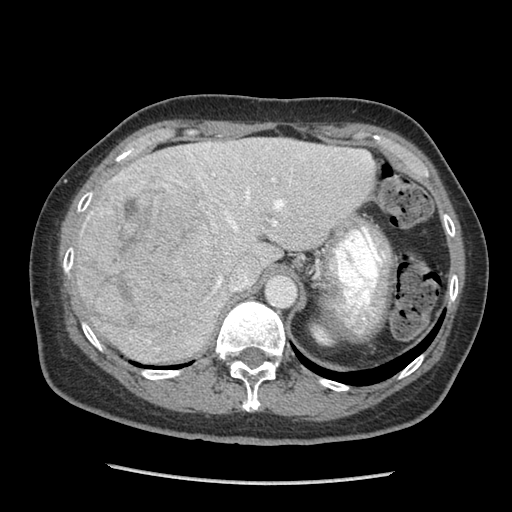
Contrast-enhanced abdominal CT (liver protocol), one axial slice; position 62 of 105 along the scan axis; reconstruction kernel STANDARD; 140 kVp; soft-tissue window (W 400 / L 40 HU); 2.5 mm slice thickness; 512 × 512 image matrix. Case-level facts recorded for this patient, not image findings: diagnosis: hepatocellular carcinoma (patient treated with transarterial chemoembolisation; whether this scan precedes or follows treatment is not stated here); TNM stage (as recorded): Stage-I; Child-Pugh class: A; tumour differentiation: moderately differentiated; tumour nodularity: uninodular.
Outlined on this slice (semi-automatic segmentation, software-assisted and operator-edited):
- abdominal aorta: bounding box <267,276,296,306> (left, top, right, bottom; pixels)
- liver parenchyma outside the tumour (the mass and vessels are separate outlines, so this box may not span the whole liver): <78,138,376,362>
- mass: <77,172,221,343>
- liver vessels: <114,144,371,288>